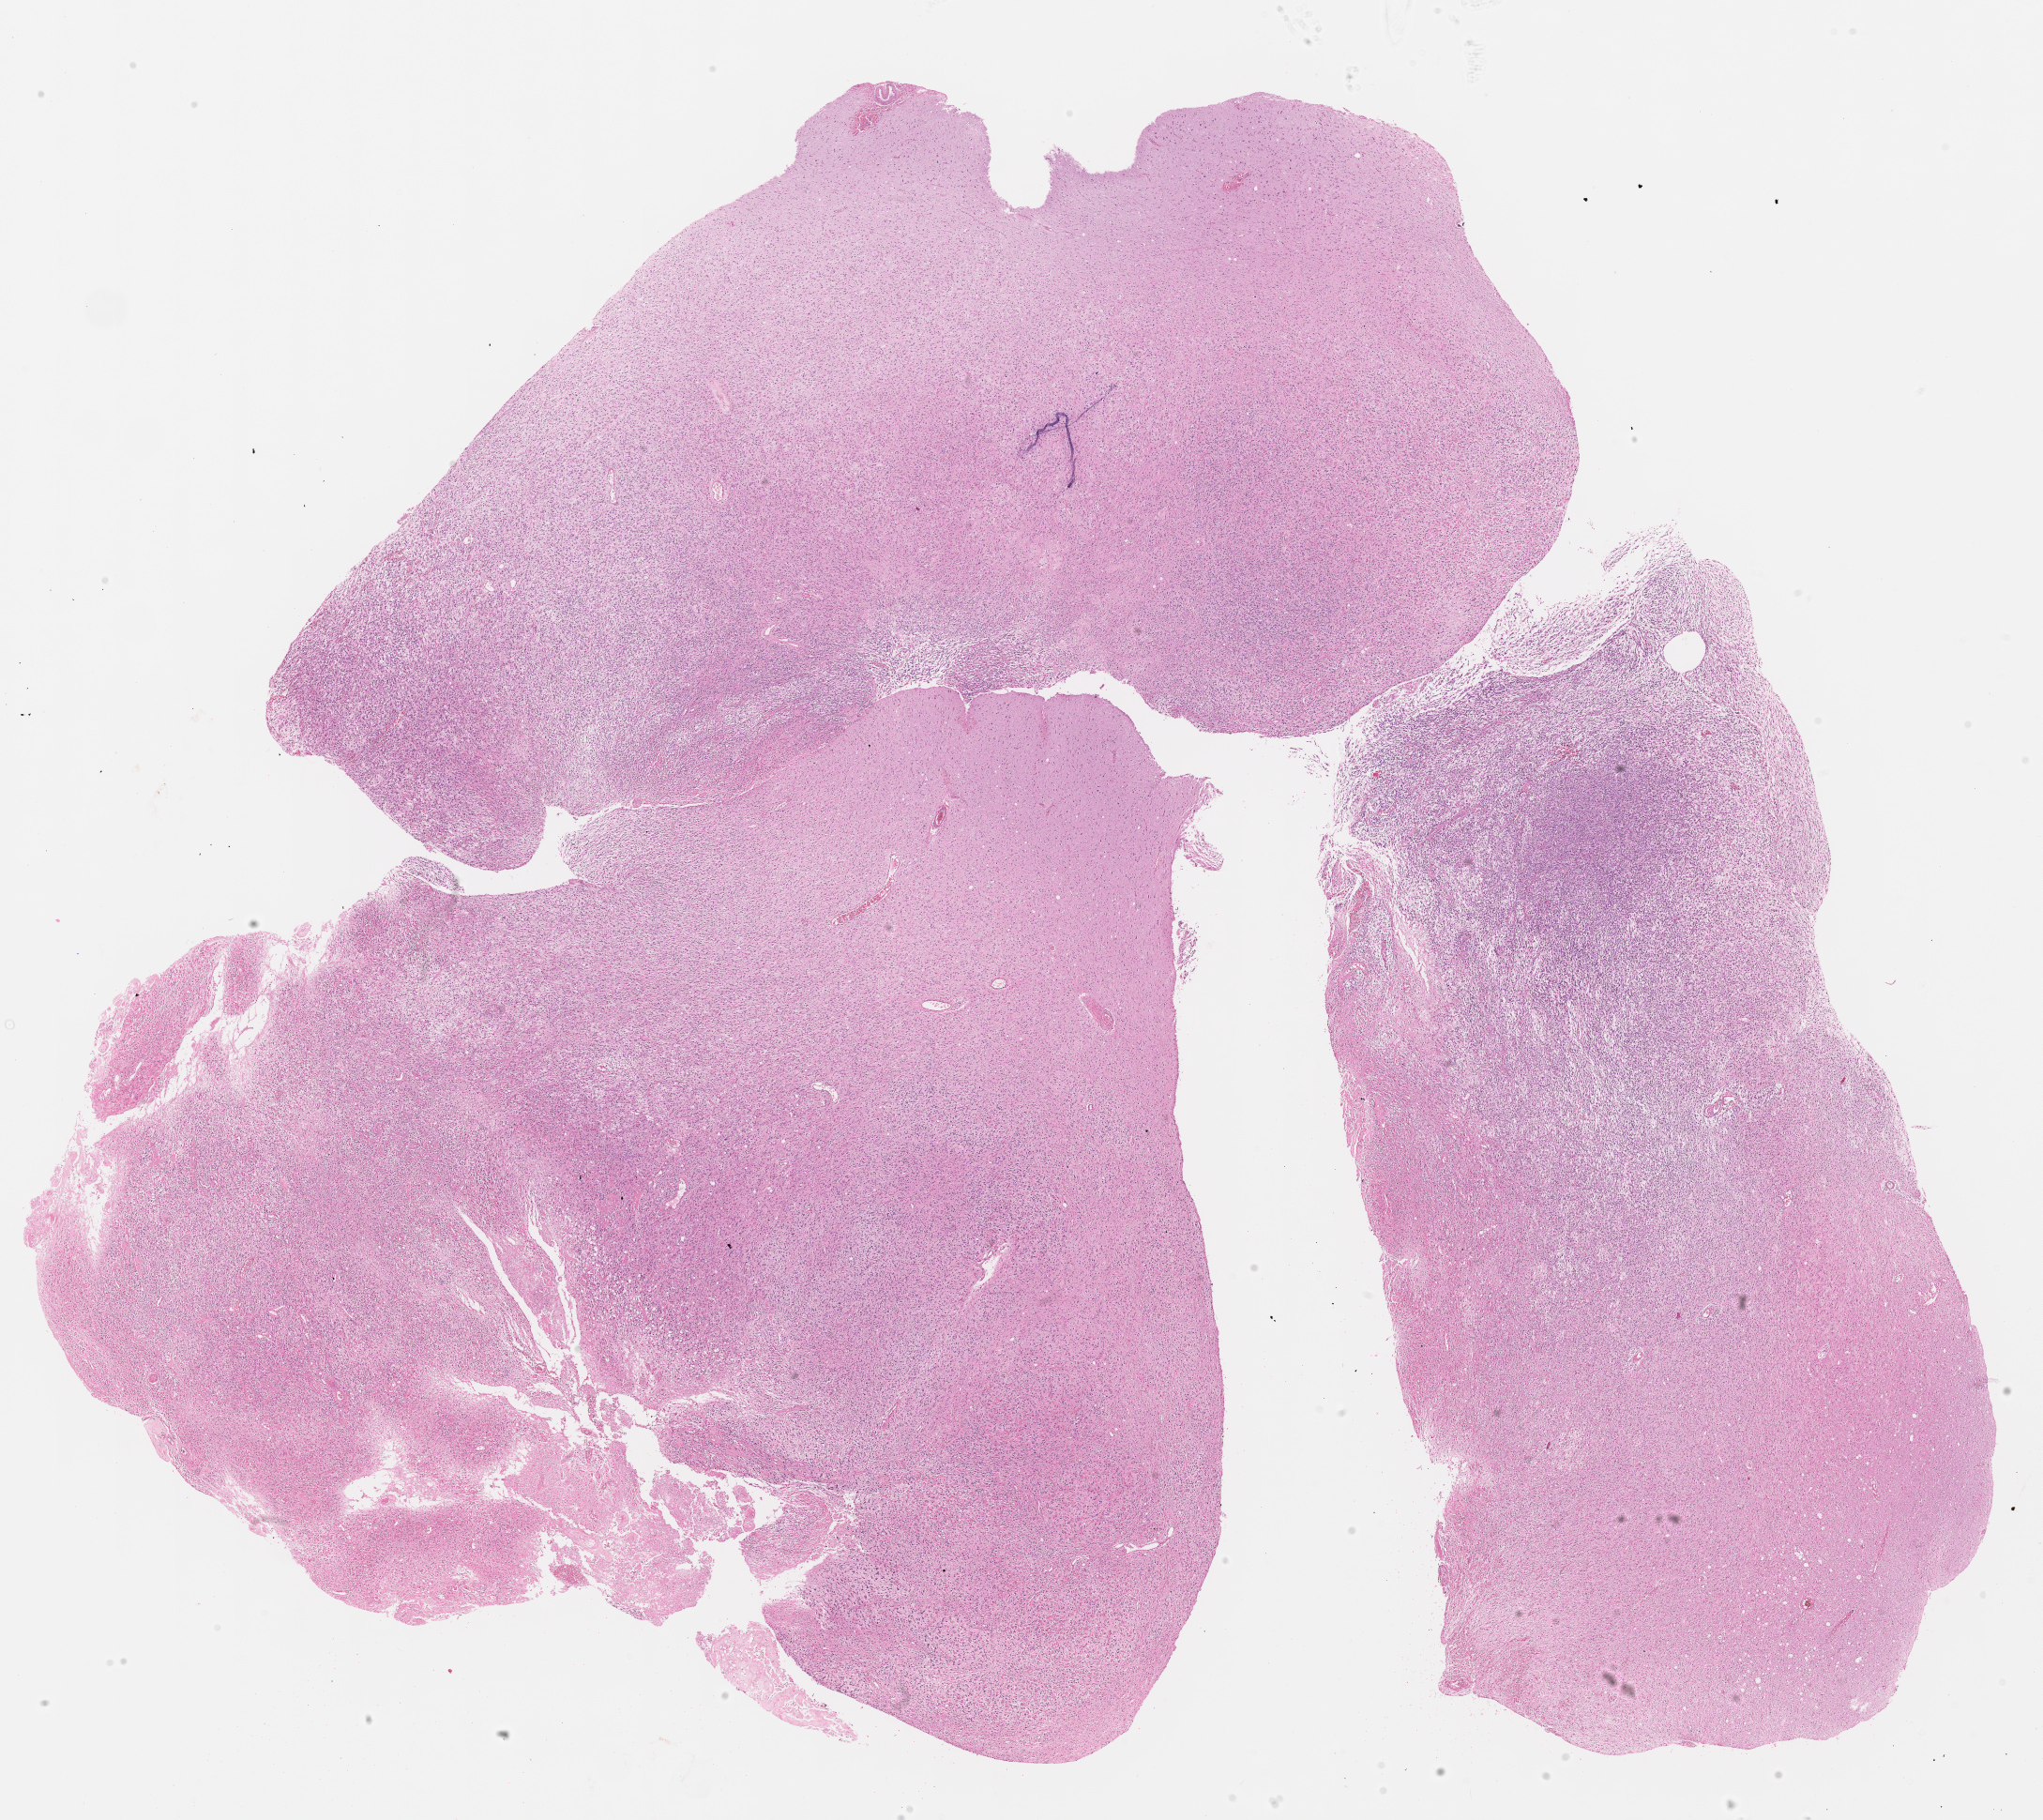
Hematoxylin and eosin (H&E) stained whole-slide image — low-resolution overview of the scanned area, about 17.7 x 15.7 mm. Formalin-fixed paraffin-embedded (FFPE) diagnostic section. Primary tumour sample from the brain. Patient: male, age at initial diagnosis 36 years.
Diagnosis: Glioblastoma.